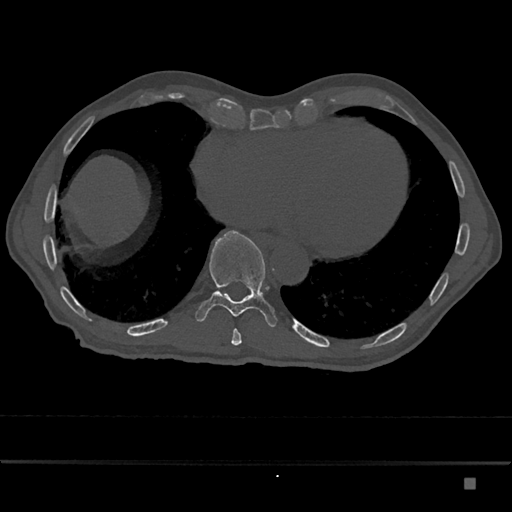
CT including the spine, one axial slice; position 747 of 797 along the scan axis; bone window (W 1800 / L 400 HU); 512 × 512 image matrix. Male patient, age 72 years. Case-level facts recorded for this patient, not image findings: primary cancer: prostate.
Annotated regions visible in this slice (semi-automatically segmented with operator editing):
- T10 vertebra: bounding box (x1, y1, x2, y2) in pixels: (196, 230, 278, 327)
- T9 vertebra: (231, 329, 242, 346)